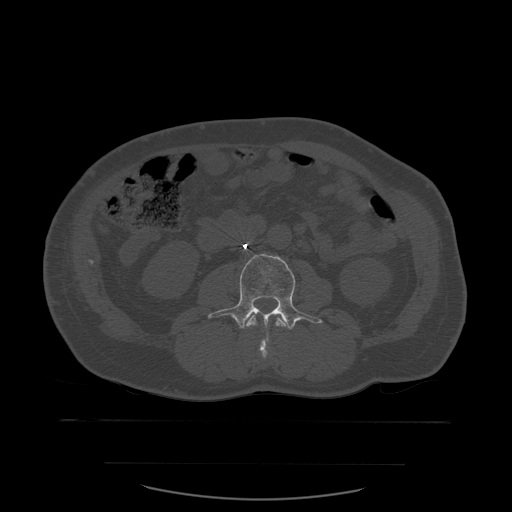
CT including the spine, one axial slice; slice 198 of 590 in the series (ordered by position); bone window (W 1800 / L 400 HU); 512 × 512 image matrix, field of view 479 × 479 mm. Patient age 71 years. Case-level facts recorded for this patient, not image findings: primary cancer: lung.
Annotated regions visible in this slice (semi-automatically segmented with operator editing):
- L2 vertebra: bounding box (x1, y1, x2, y2) in pixels: (244, 309, 291, 359)
- L3 vertebra: (208, 254, 323, 338)